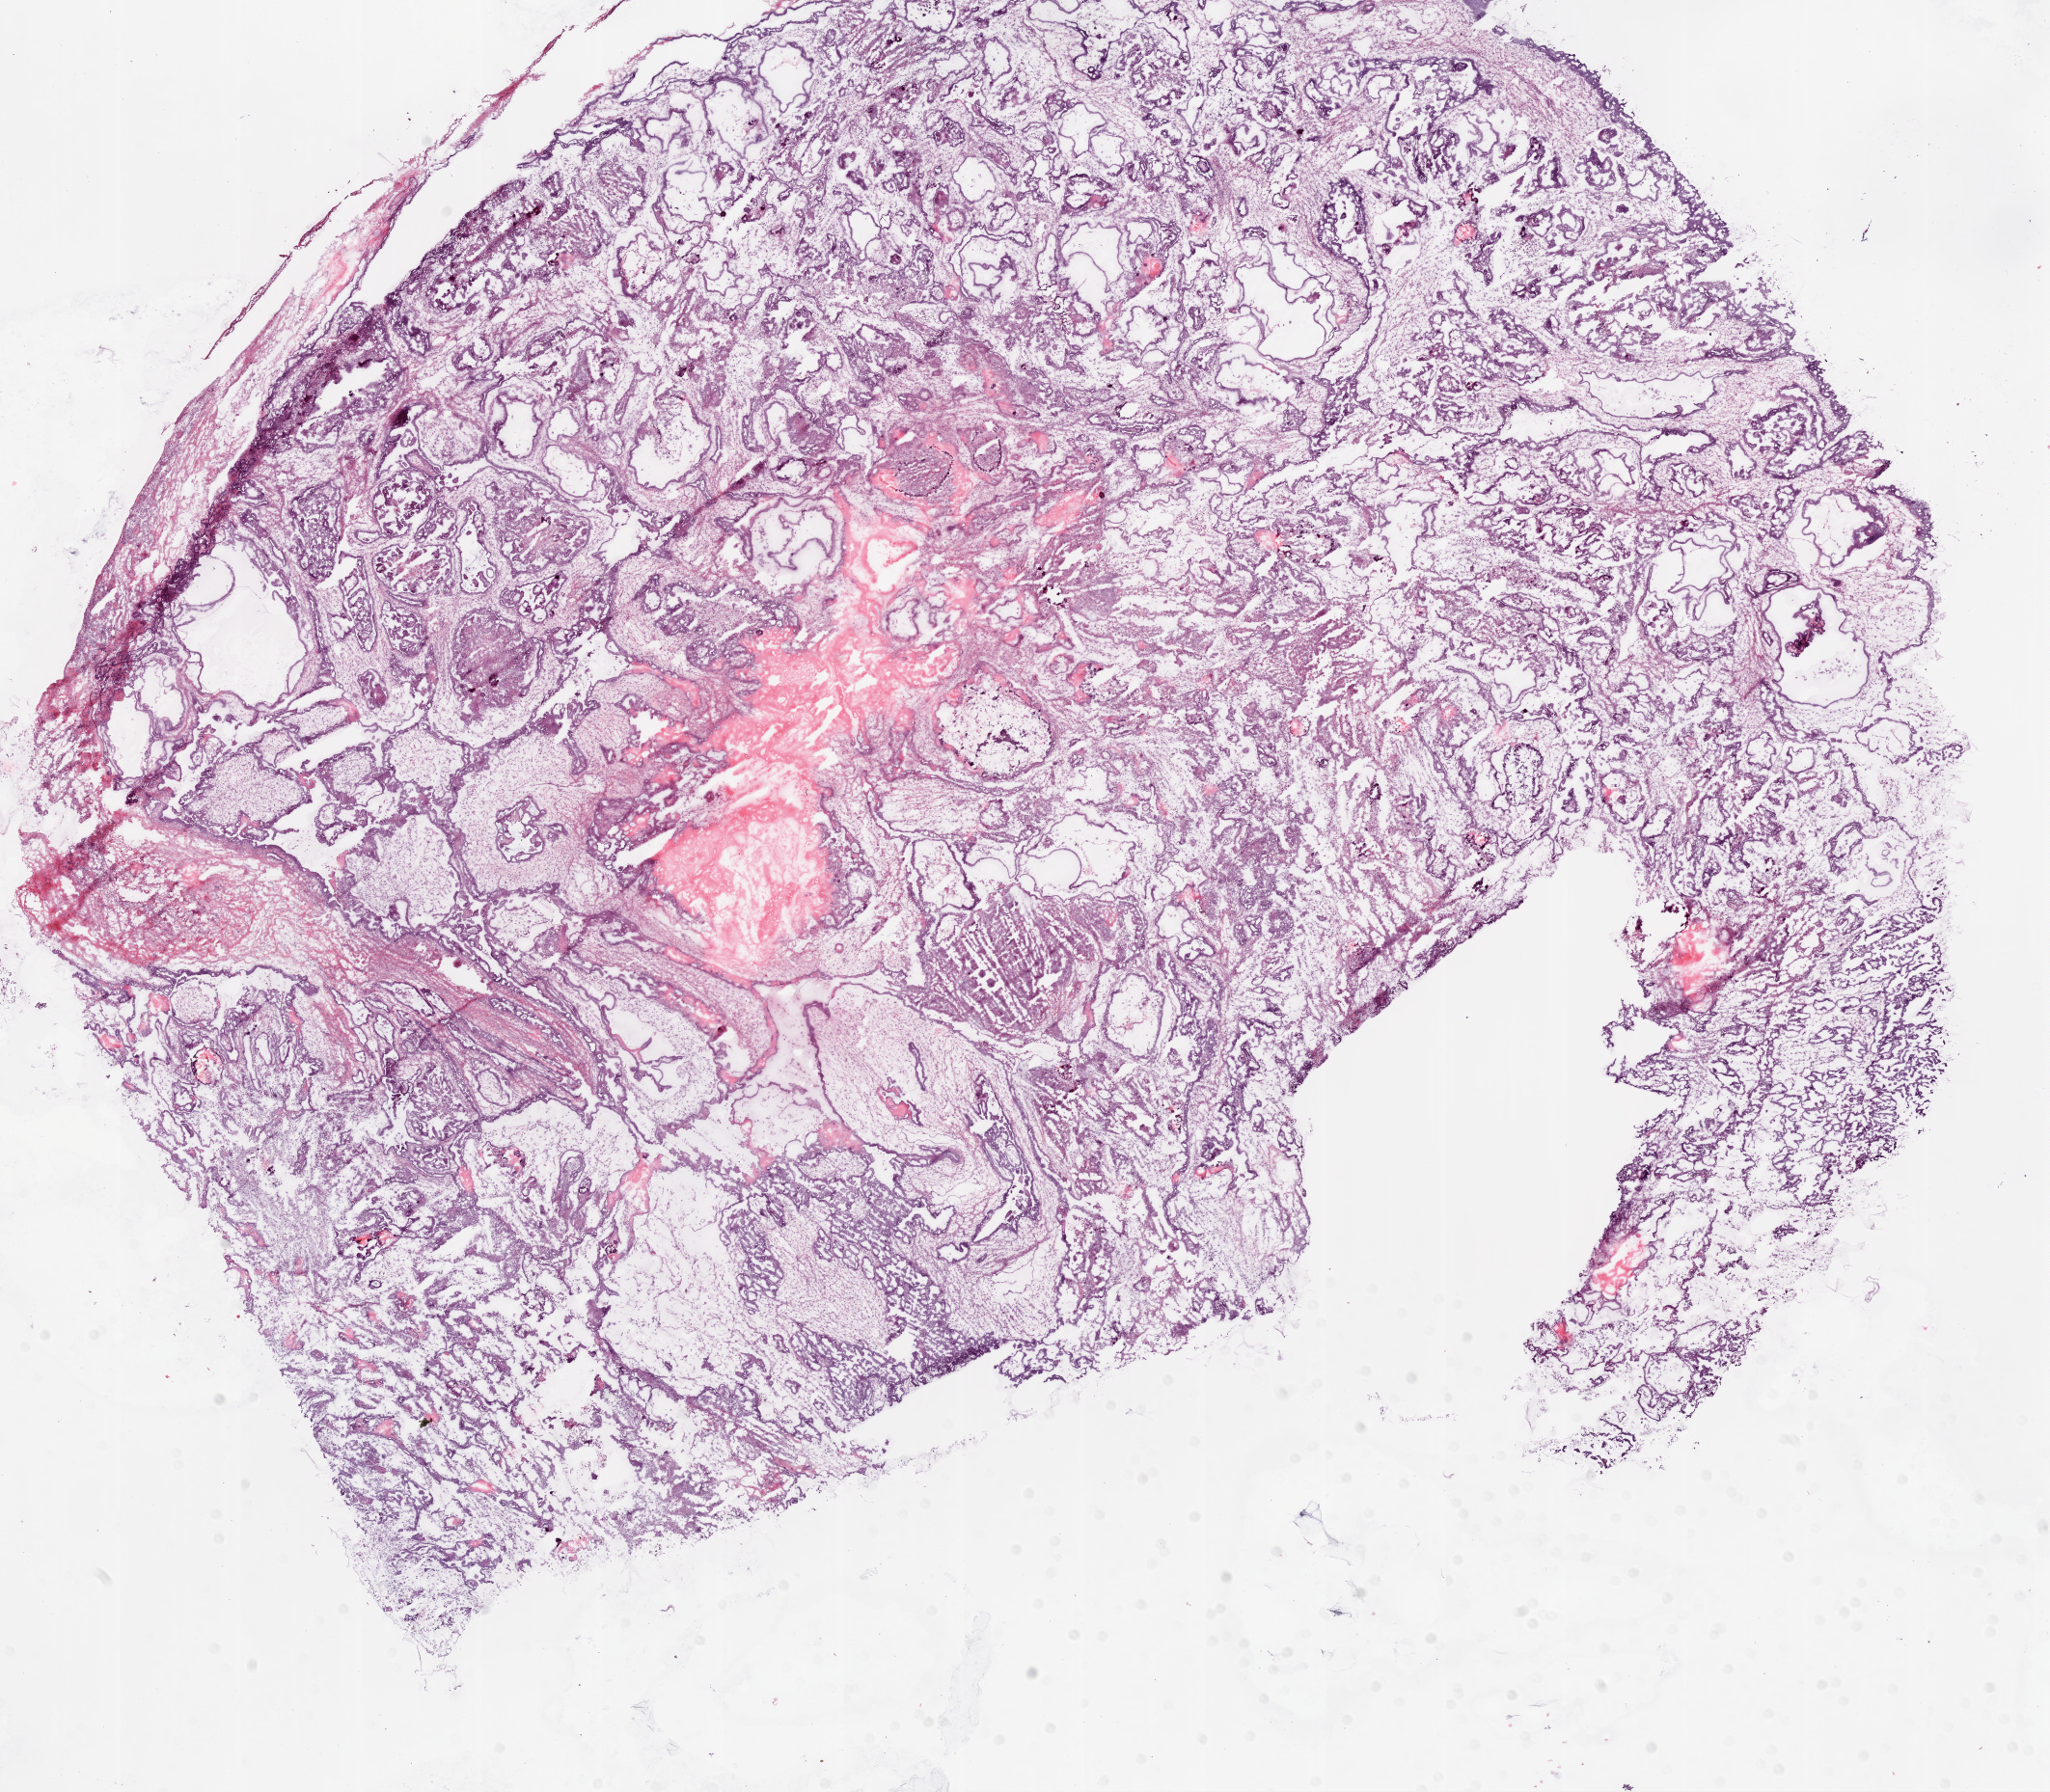
H&E-stained whole-slide image, shown as a low-resolution overview of the whole scanned area (about 17.1 x 14.9 mm, from a 20x scan). Frozen section. Sample: primary tumour, ovary. Patient: female, age at initial diagnosis 54 years. Pathologist review of this section (percent, as recorded): tumour cells 60%, tumour nuclei 80%.
Diagnosis: Serous cystadenocarcinoma, NOS.